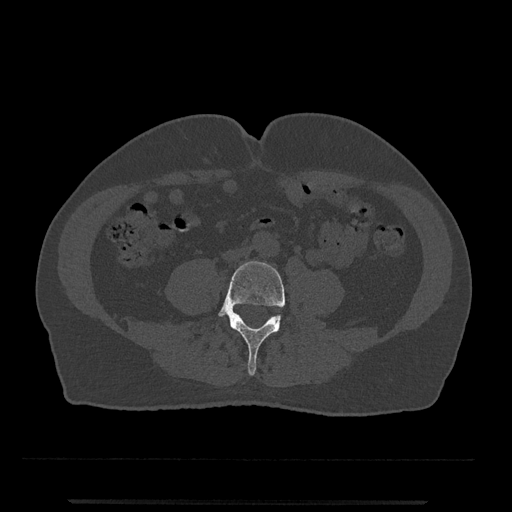
CT including the spine, one axial slice. Position 133 of 797 along the scan axis. Reconstruction kernel Br40s/3. Bone window (W 1800 / L 400 HU). 0.5 mm slice thickness. 512 × 512 image matrix, field of view 419 × 419 mm. Patient: male, 63 years. From the clinical record (not read from this slice): primary cancer: prostate.
Structures marked on this image (semi-automatically segmented with operator editing):
- L4 vertebra: bounding box <218,261,289,376> (left, top, right, bottom; pixels)